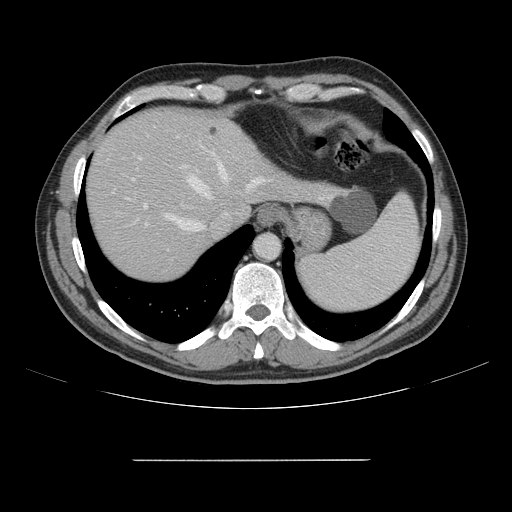
Contrast-enhanced abdominal CT, one axial slice. Slice 128 of 164 in the series (ordered by position). 120 kVp. Intravenous contrast given. Soft-tissue window (W 400 / L 40 HU). 2.5 mm slice thickness. 512 × 512 image matrix, field of view 404 × 404 mm. Male patient, age 54 years. From the clinical record (not read from this slice): diagnosis: colorectal cancer liver metastases, imaged before liver resection; multiple liver metastases: yes; largest metastasis: 1 cm; chemotherapy before resection: yes.
Outlined on this slice (manually delineated by an expert):
- hepatic veins: bounding box [x1, y1, x2, y2] px = [137, 153, 262, 231]
- liver: [88, 109, 332, 280]
- planned liver remnant (the part of the liver to remain after resection): [88, 109, 255, 280]
- portal vein (with intrahepatic branches): [132, 152, 213, 226]